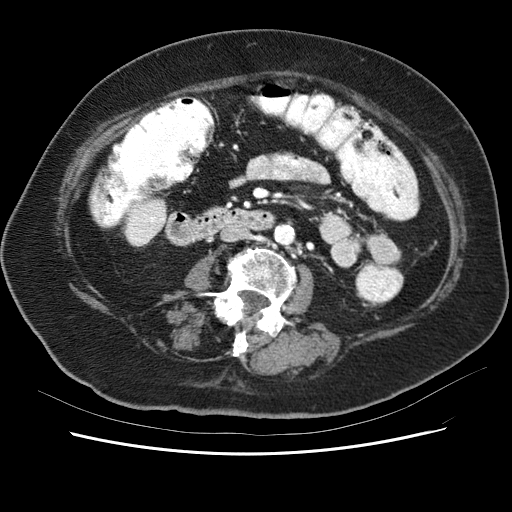
Contrast-enhanced abdominal CT (liver protocol), one axial slice; slice 6 of 62 in the series (ordered by position); reconstruction kernel STANDARD; 120 kVp; soft-tissue window (W 400 / L 40 HU); 512 × 512 image matrix, field of view 340 × 340 mm. Case-level facts recorded for this patient, not image findings: diagnosis: hepatocellular carcinoma (patient treated with transarterial chemoembolisation; whether this scan precedes or follows treatment is not stated here); TNM stage (as recorded): Stage-I; Child-Pugh class: B; tumour nodularity: uninodular; tumour size: 5.3 cm.
Annotated regions visible in this slice (semi-automatically segmented with operator editing):
- liver parenchyma outside the tumour (the mass and vessels are separate outlines, so this box may not span the whole liver): bounding box (x1, y1, x2, y2) in pixels: (127, 196, 148, 214)
- liver vessels: (130, 207, 135, 212)